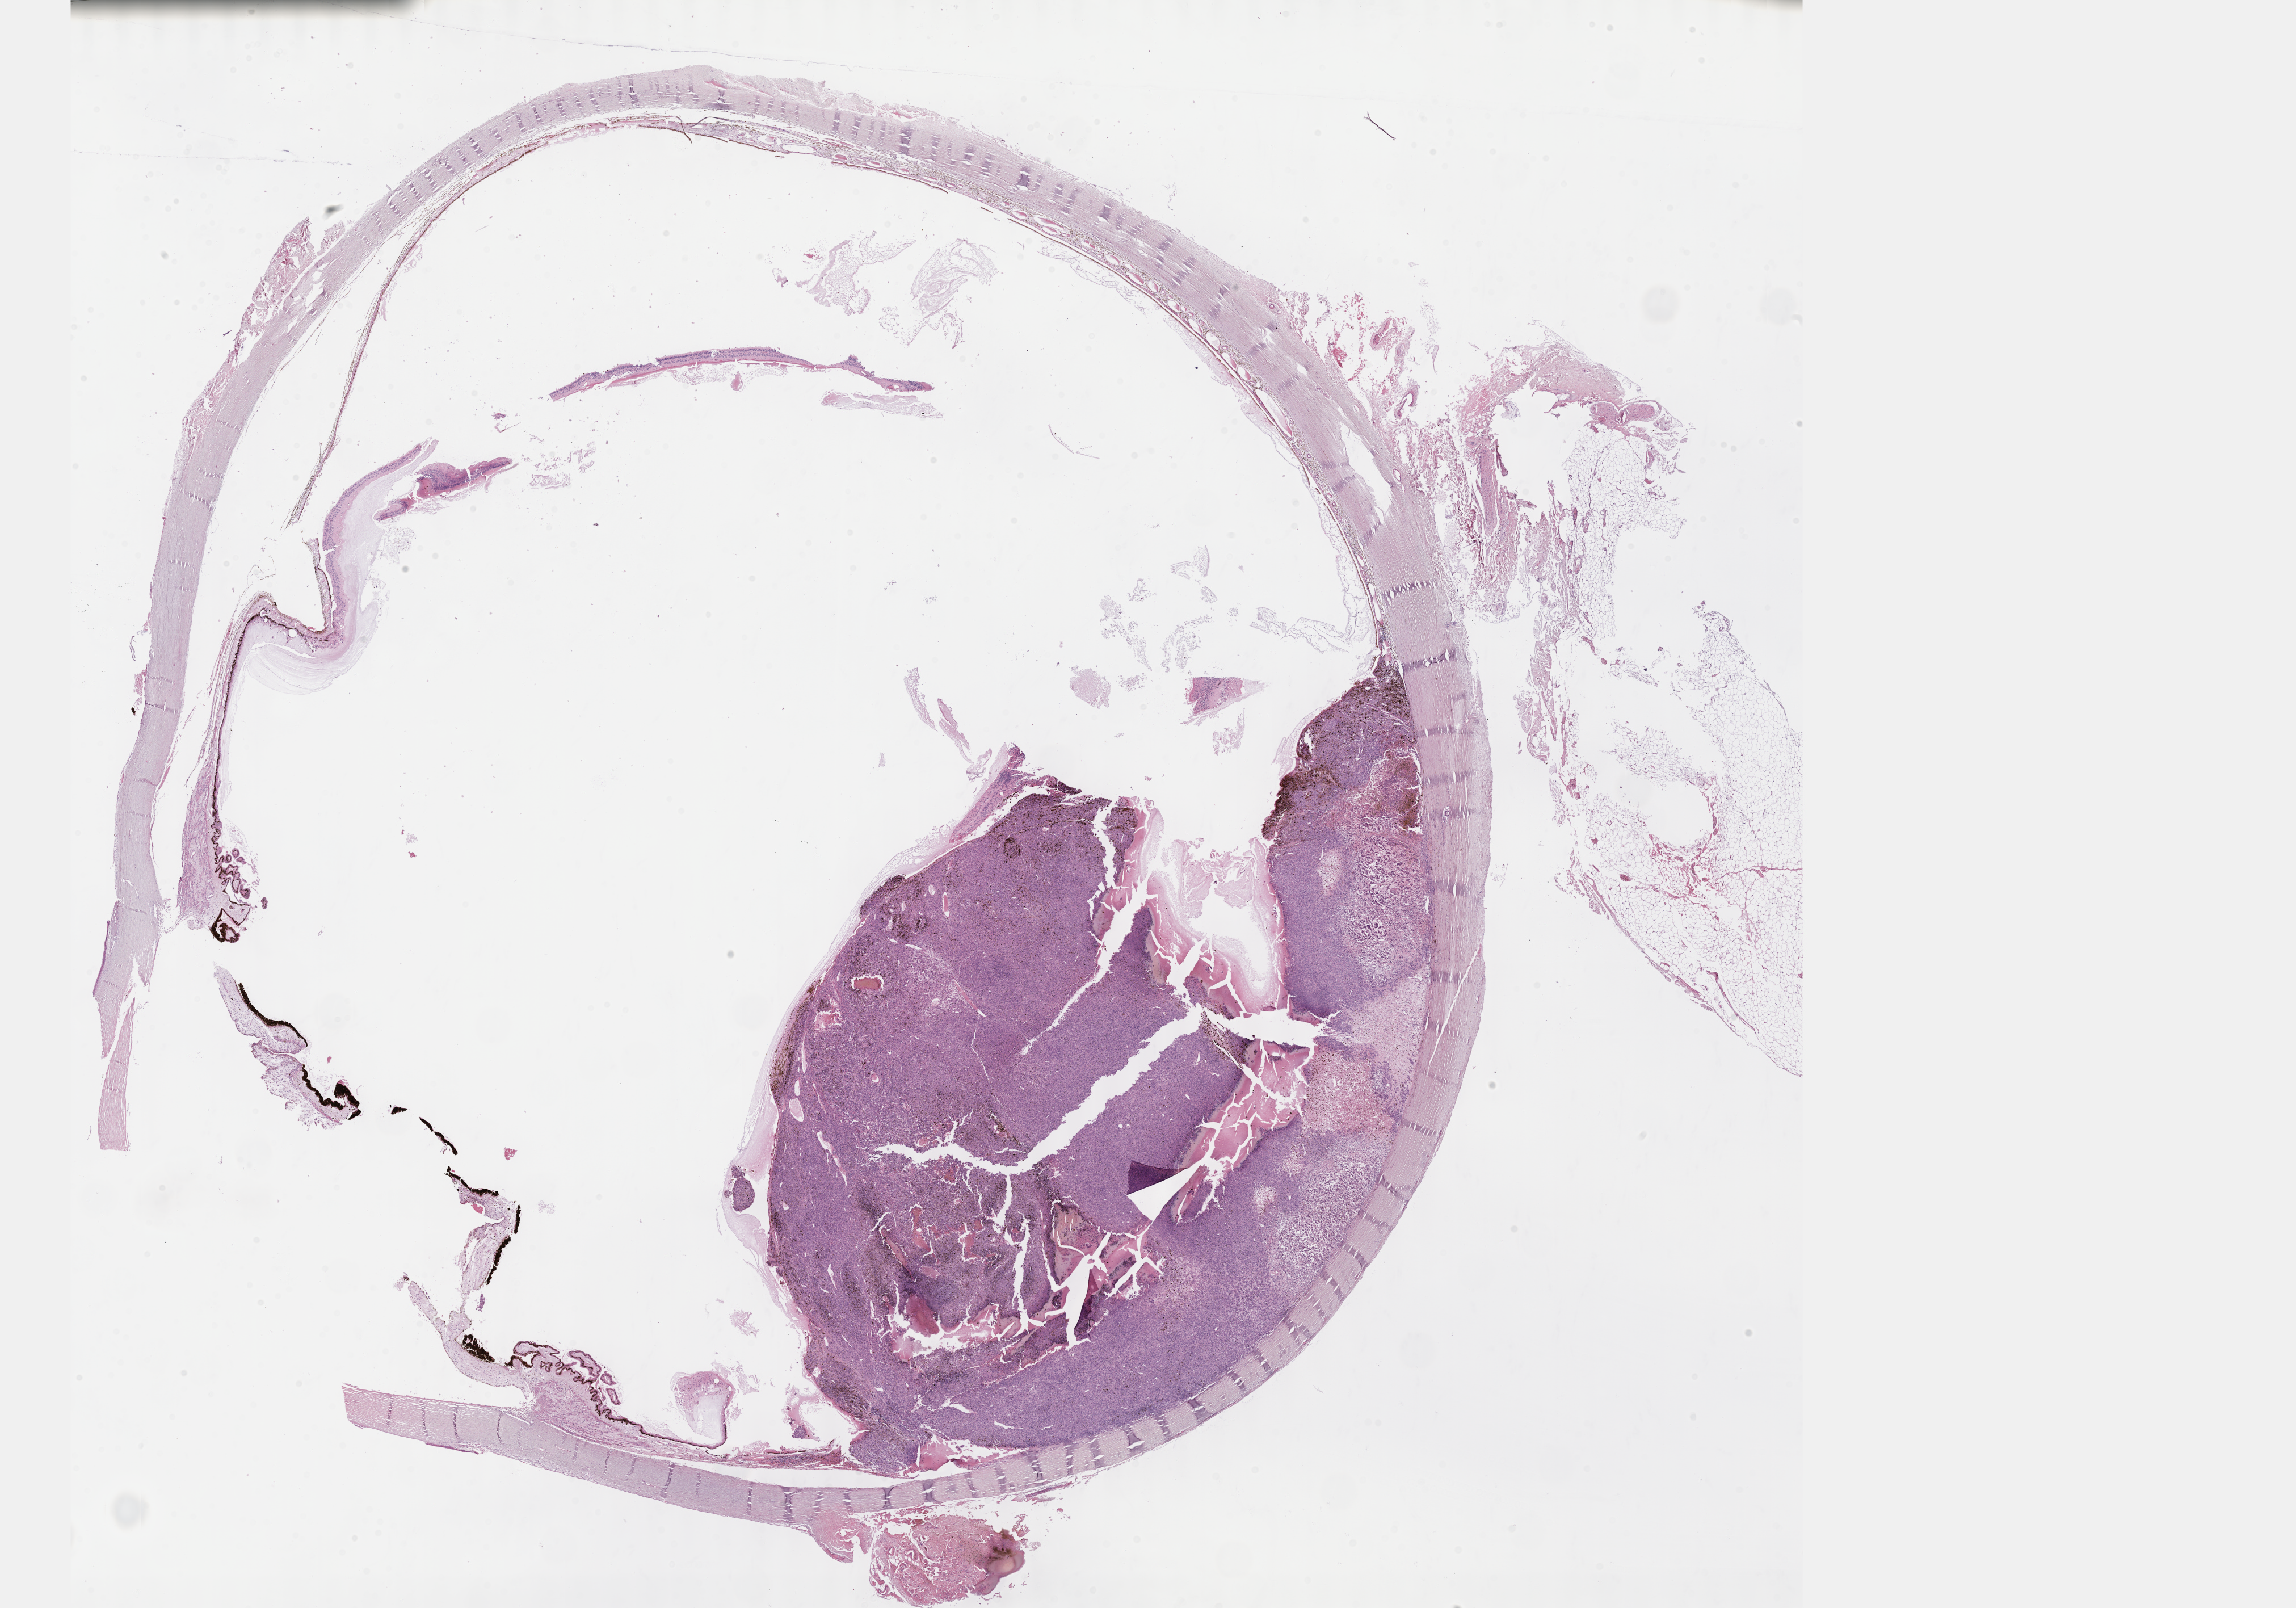
H&E-stained whole-slide image, shown as a low-resolution overview of the whole scanned area (about 32.7 x 22.9 mm). Formalin-fixed paraffin-embedded (FFPE) diagnostic section. Uvea, primary tumour sample. Patient: male, age at initial diagnosis 86 years.
Pathologic diagnosis: Epithelioid cell melanoma. AJCC pathologic stage: IIB (7th edition).